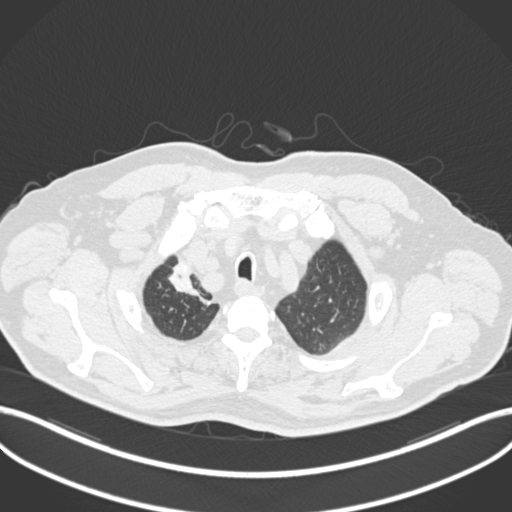
Chest CT, one axial slice. Position 180 of 255 along the scan axis. 120 kVp. Lung window (W 1500 / L -600 HU). 512 × 512 image matrix, field of view 400 × 400 mm. Patient: male, 60 years. From the clinical record (not read from this slice): clinical TNM (as recorded): T1b N1 M0.
Outlined on this slice (rectangle marked by the reading radiologist):
- lung tumour (recorded histology: squamous cell carcinoma): box from (x=164, y=261) to (x=206, y=307) px